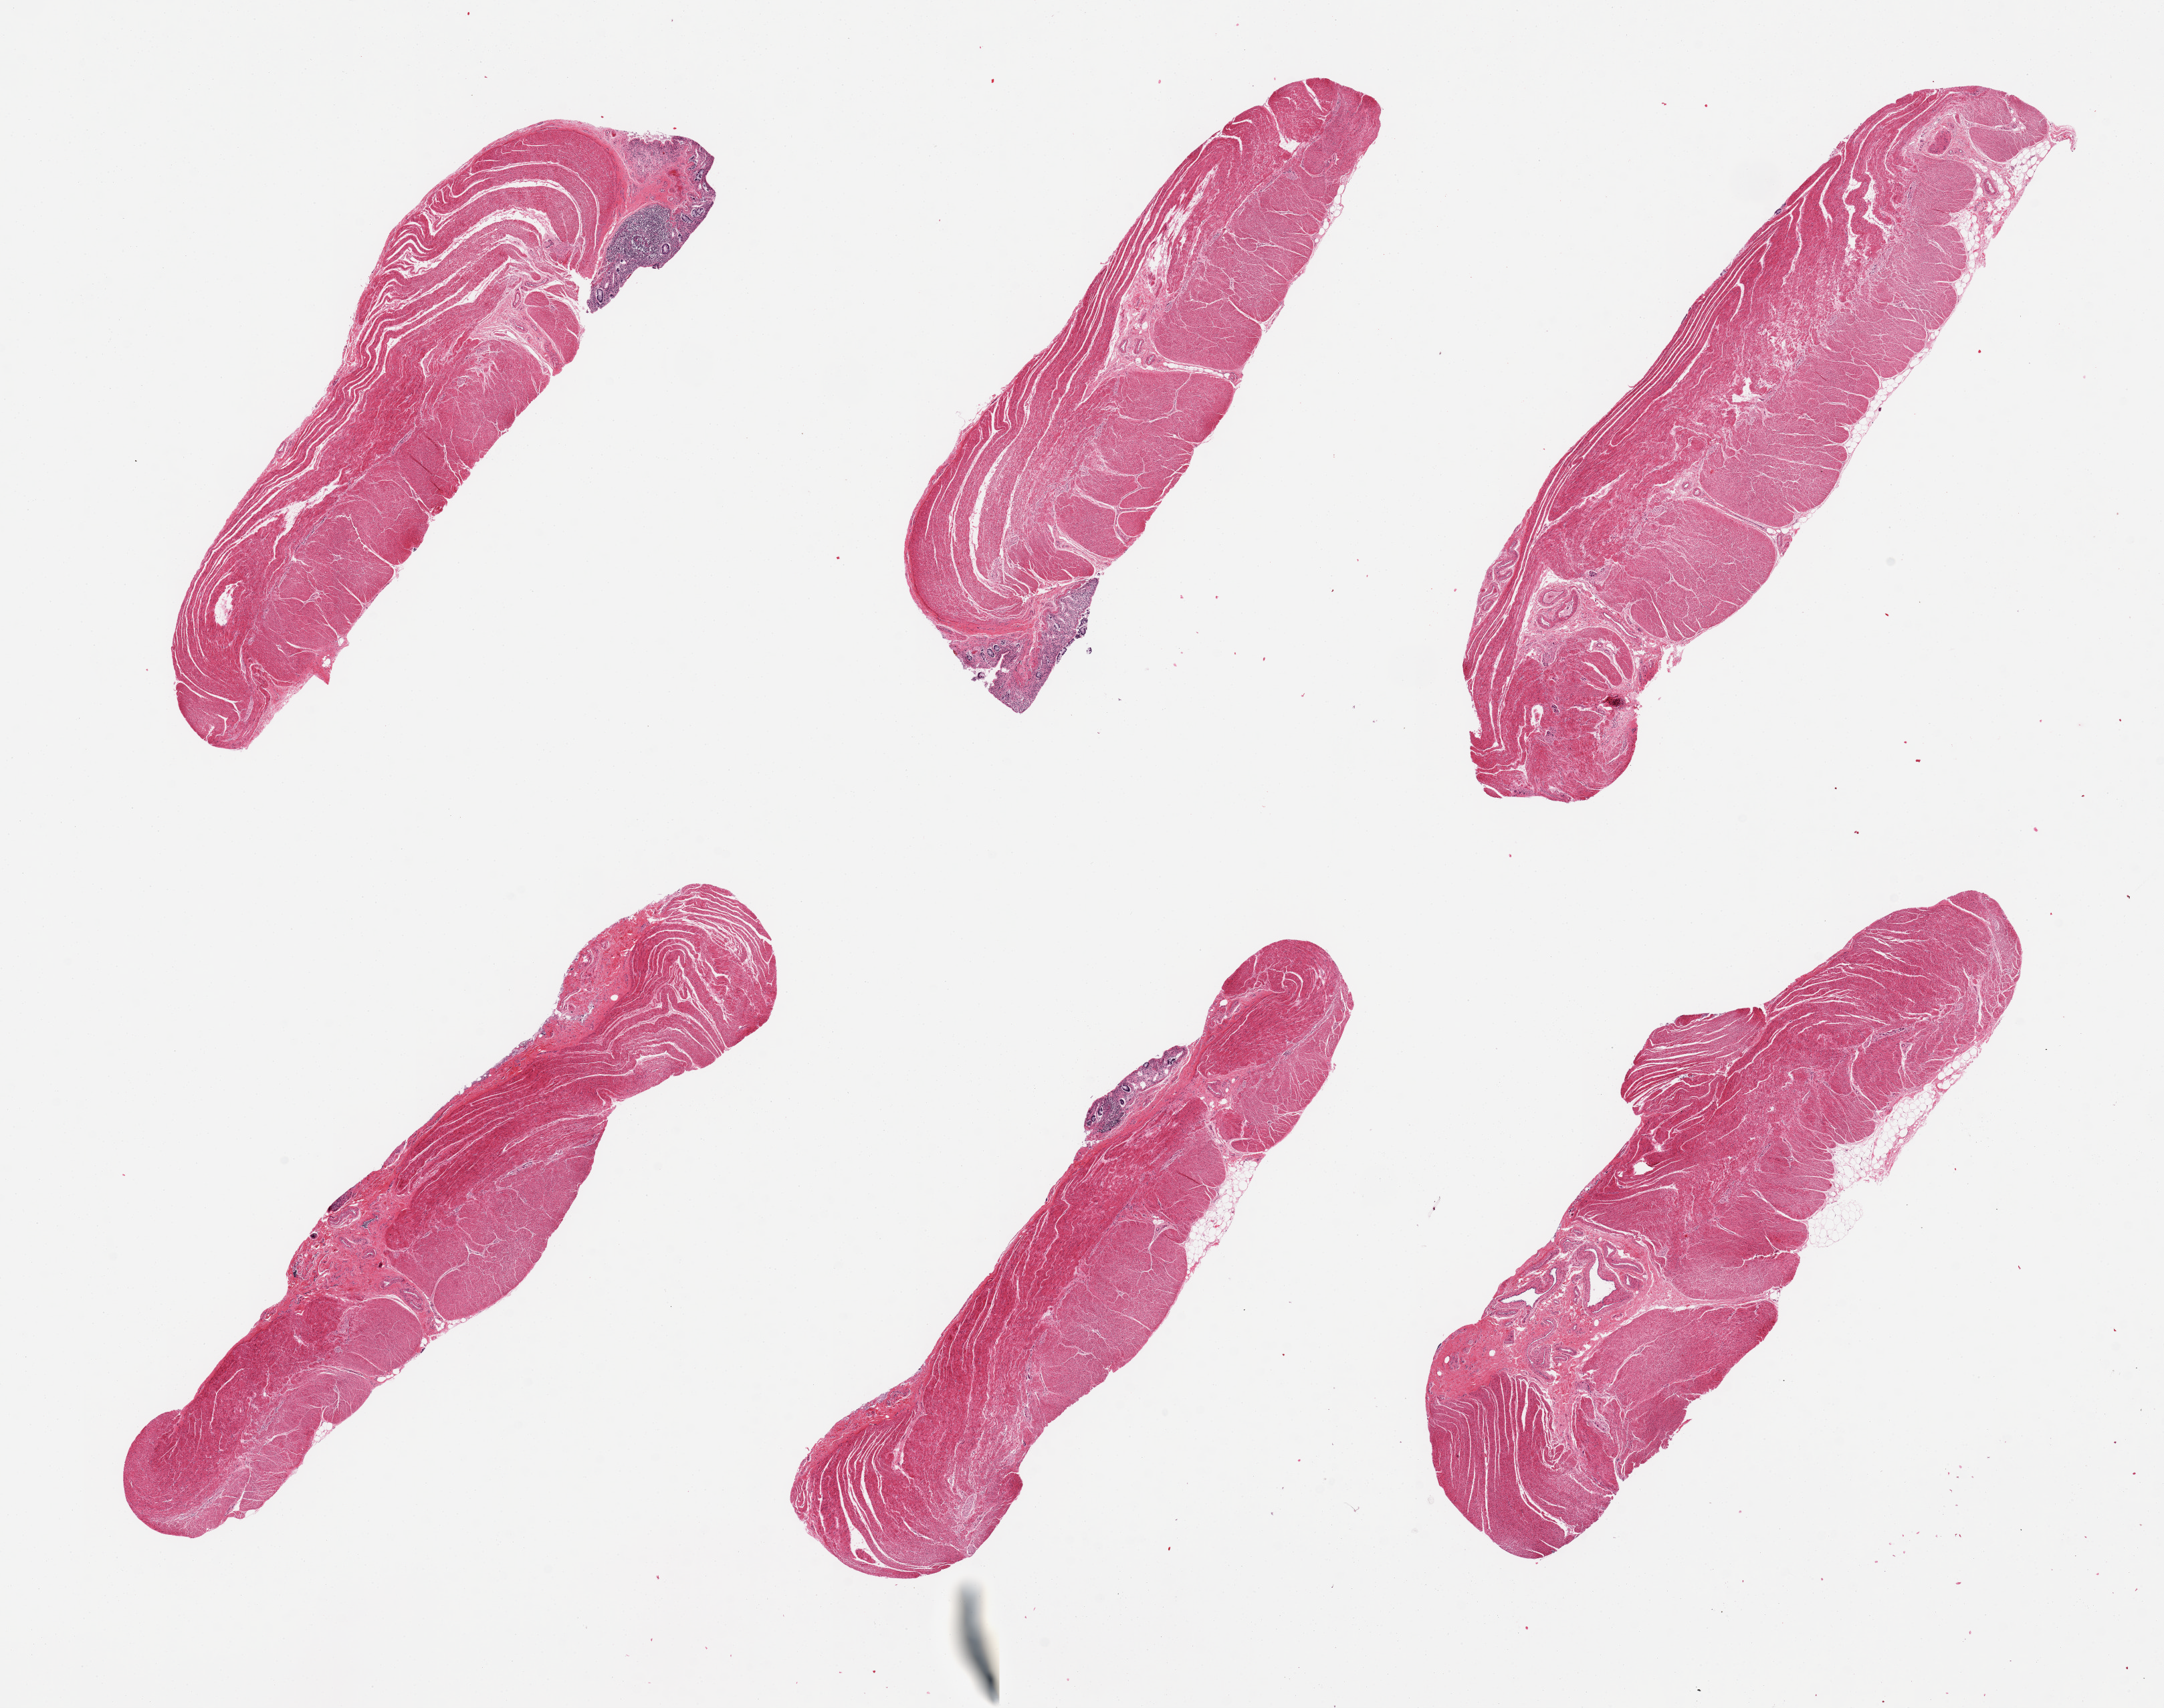
Digitized H&E-stained section, a low-resolution overview of the entire scanned area, about 25.6 x 20.2 mm (slide scanned at 20x); PAXgene-fixed, paraffin-embedded tissue; sampled site (target tissue): sigmoid colon; tissue donor sample. Male donor.
* reviewer comment on this tissue sample: 6 pieces, predominantly muscularis (target) with few strips of markedly autolyzed mucosa (not target)